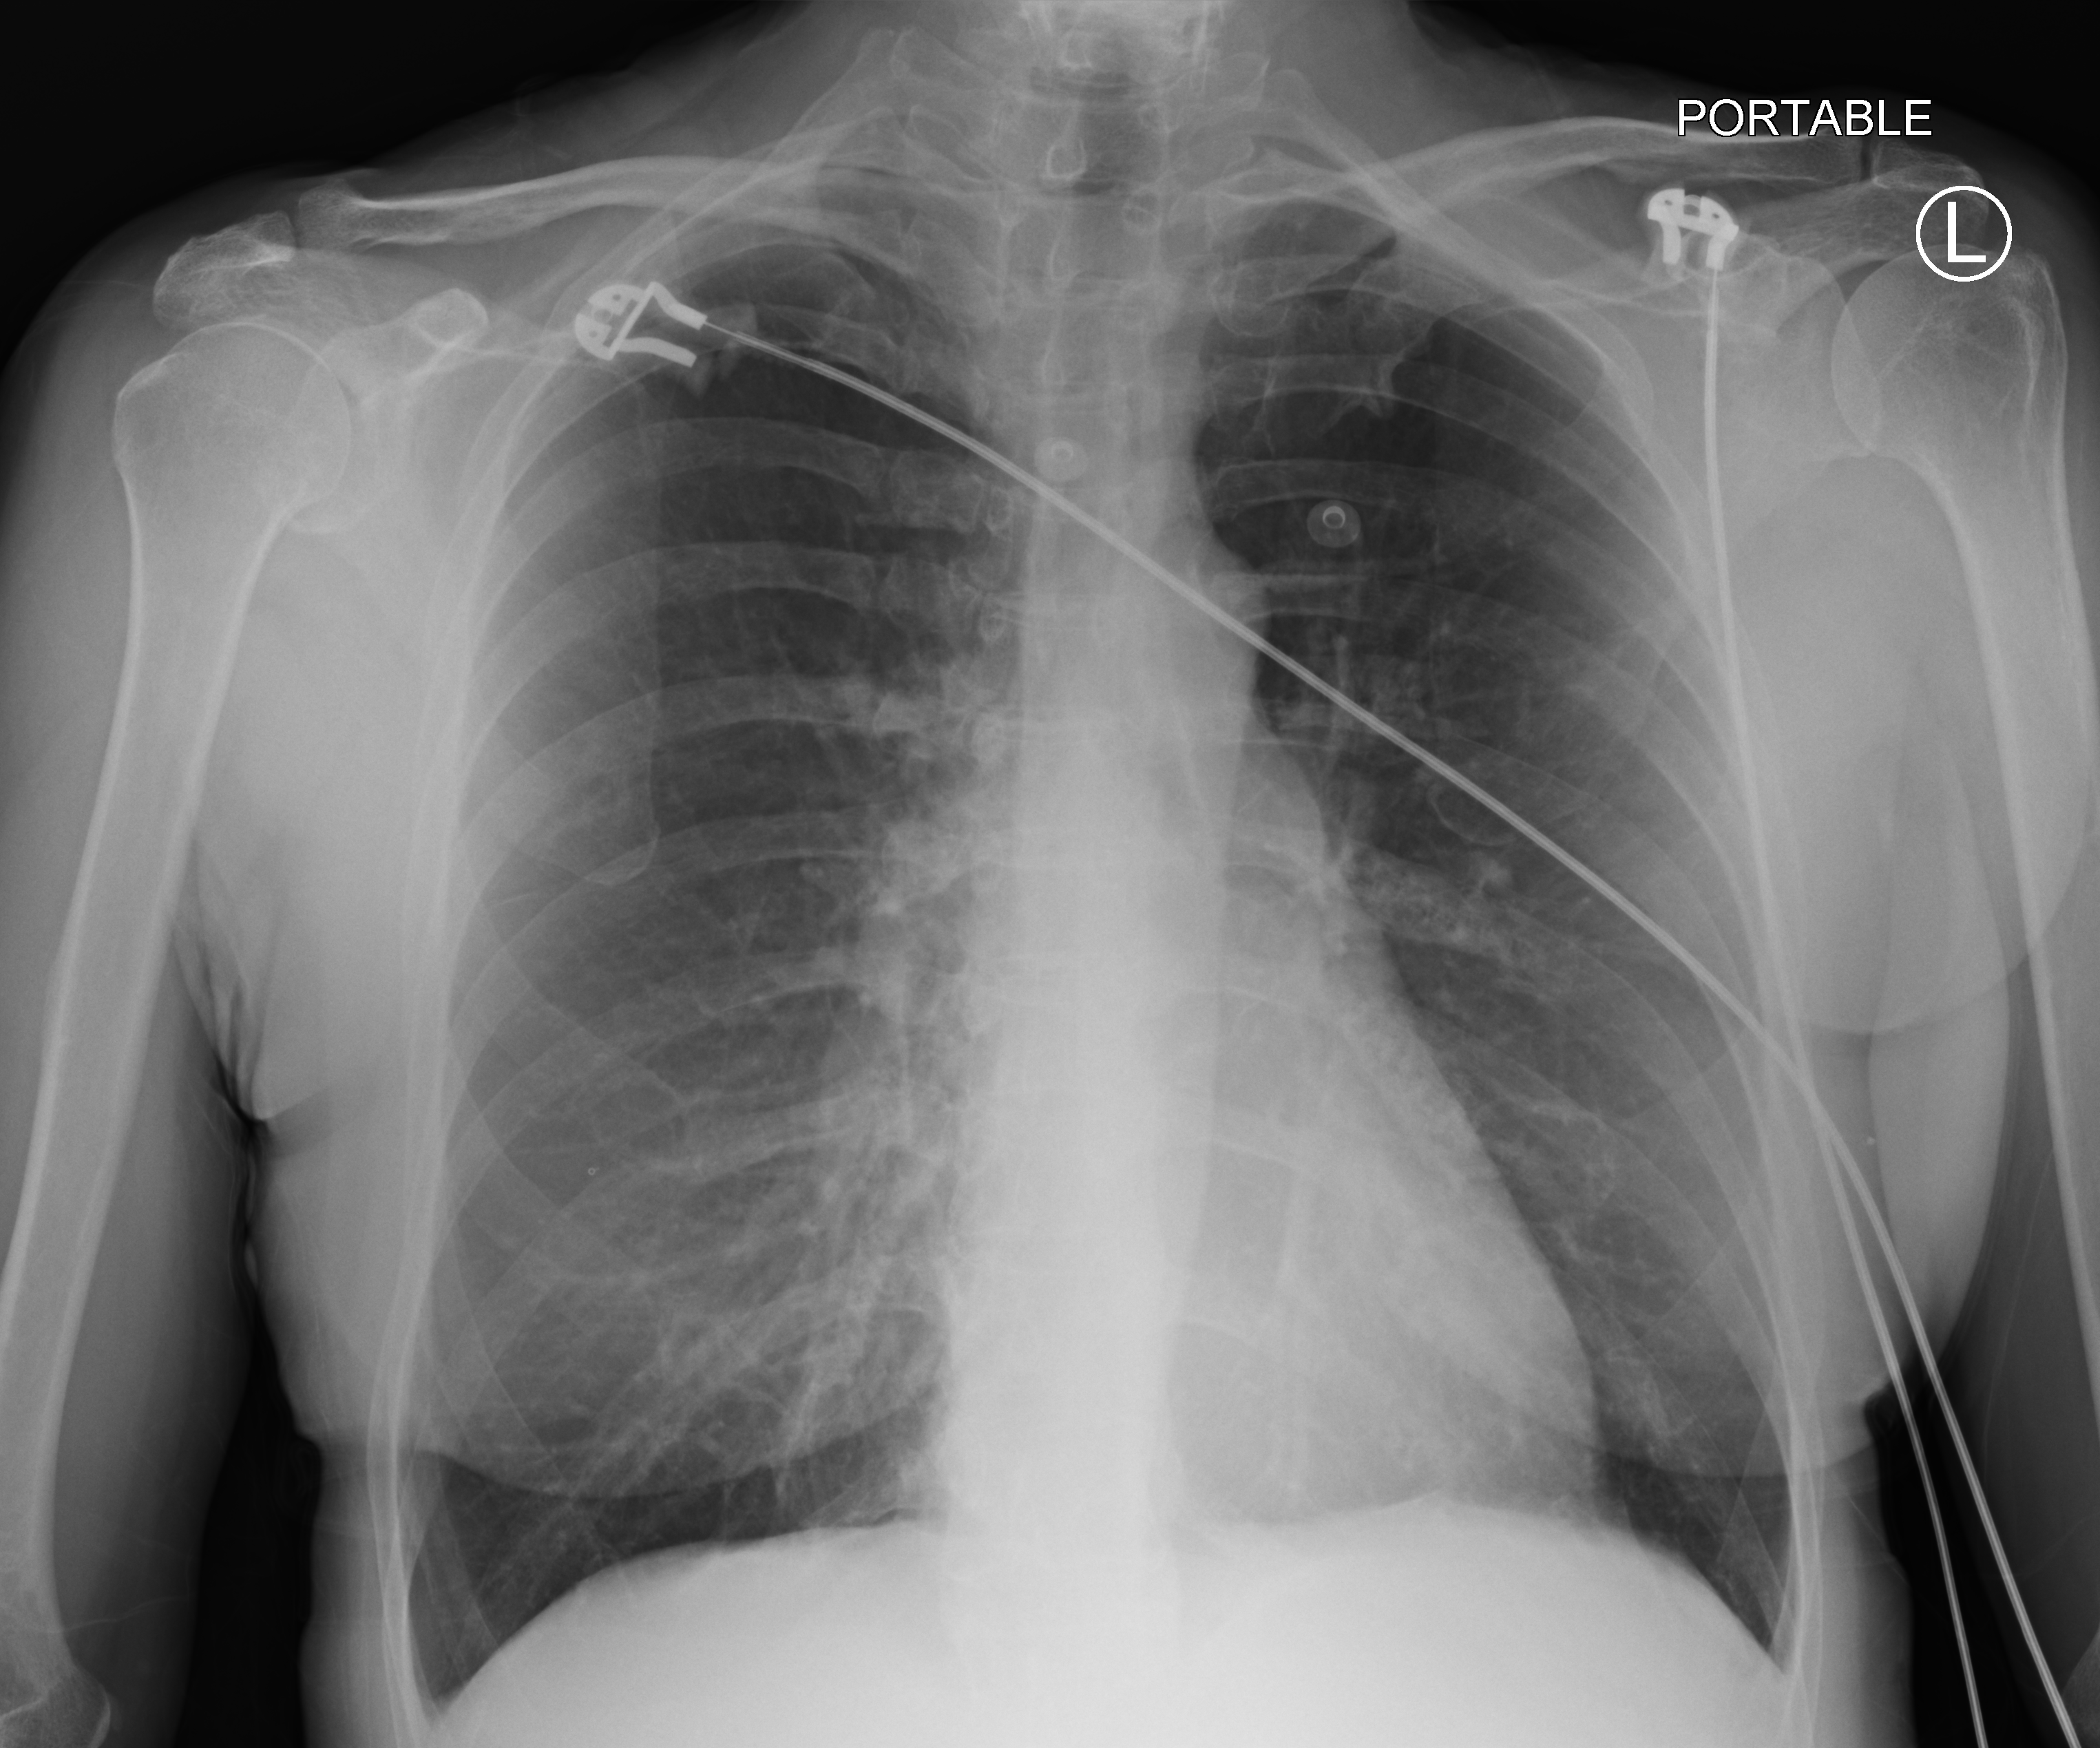
Bedside chest radiograph (computed radiography); anteroposterior (AP) projection. Patient hospitalised with COVID-19; female, aged 18–59 years.
Admission-level facts for this patient (not findings on this image; timing relative to this image not recorded):
- admitted to intensive care during this hospital stay: no